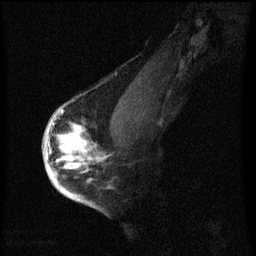
Breast MRI (dynamic contrast-enhanced), one sagittal slice. Position 42 of 60 along the scan axis. Dynamic contrast-enhanced series, image 2 of 3 at this slice position (ordered by acquisition). 1.5 T. TE 4.2 ms, TR 8 ms. 2 mm slice thickness. 256 × 256 image matrix. Patient: female, 56 years.
Outlined on this slice (semi-automatically segmented with operator editing):
- analysis volume of interest (the breast-tissue region the enhancement analysis was run in; not a lesion): bounding box [x1, y1, x2, y2] px = [44, 110, 109, 193]
- tumour enhancement mask (voxels above the 70 % enhancement threshold inside the analysis volume of interest): [44, 110, 107, 193]